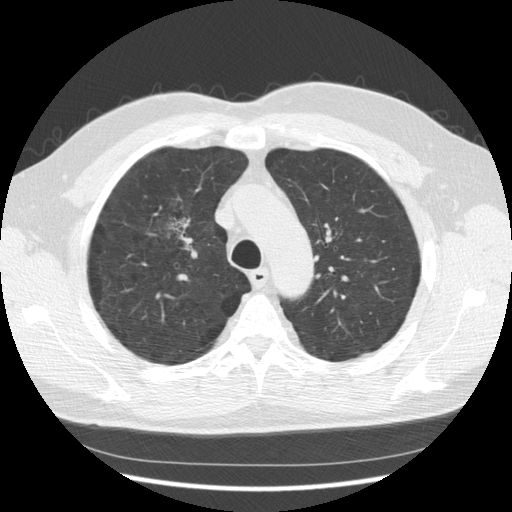
Low-dose screening chest CT, axial slice, third annual screen, lung window (W 1500 / L -600 HU), standard (soft-tissue) reconstruction kernel (STANDARD), 512 × 512 image matrix. Male participant, aged 60 years at enrolment. Former smoker at enrolment.
Expert-annotated lung lesion, bounding box <140,197,203,270> (left, top, right, bottom; pixels). Screening reader's record for this exam (one nodule recorded; not confirmed to be the boxed lesion): non-calcified nodule or mass ≥4 mm, right upper lobe, poorly defined margins, mixed attenuation, pre-existing on the prior screen: yes; interval growth: yes. Official screen result: positive, other.